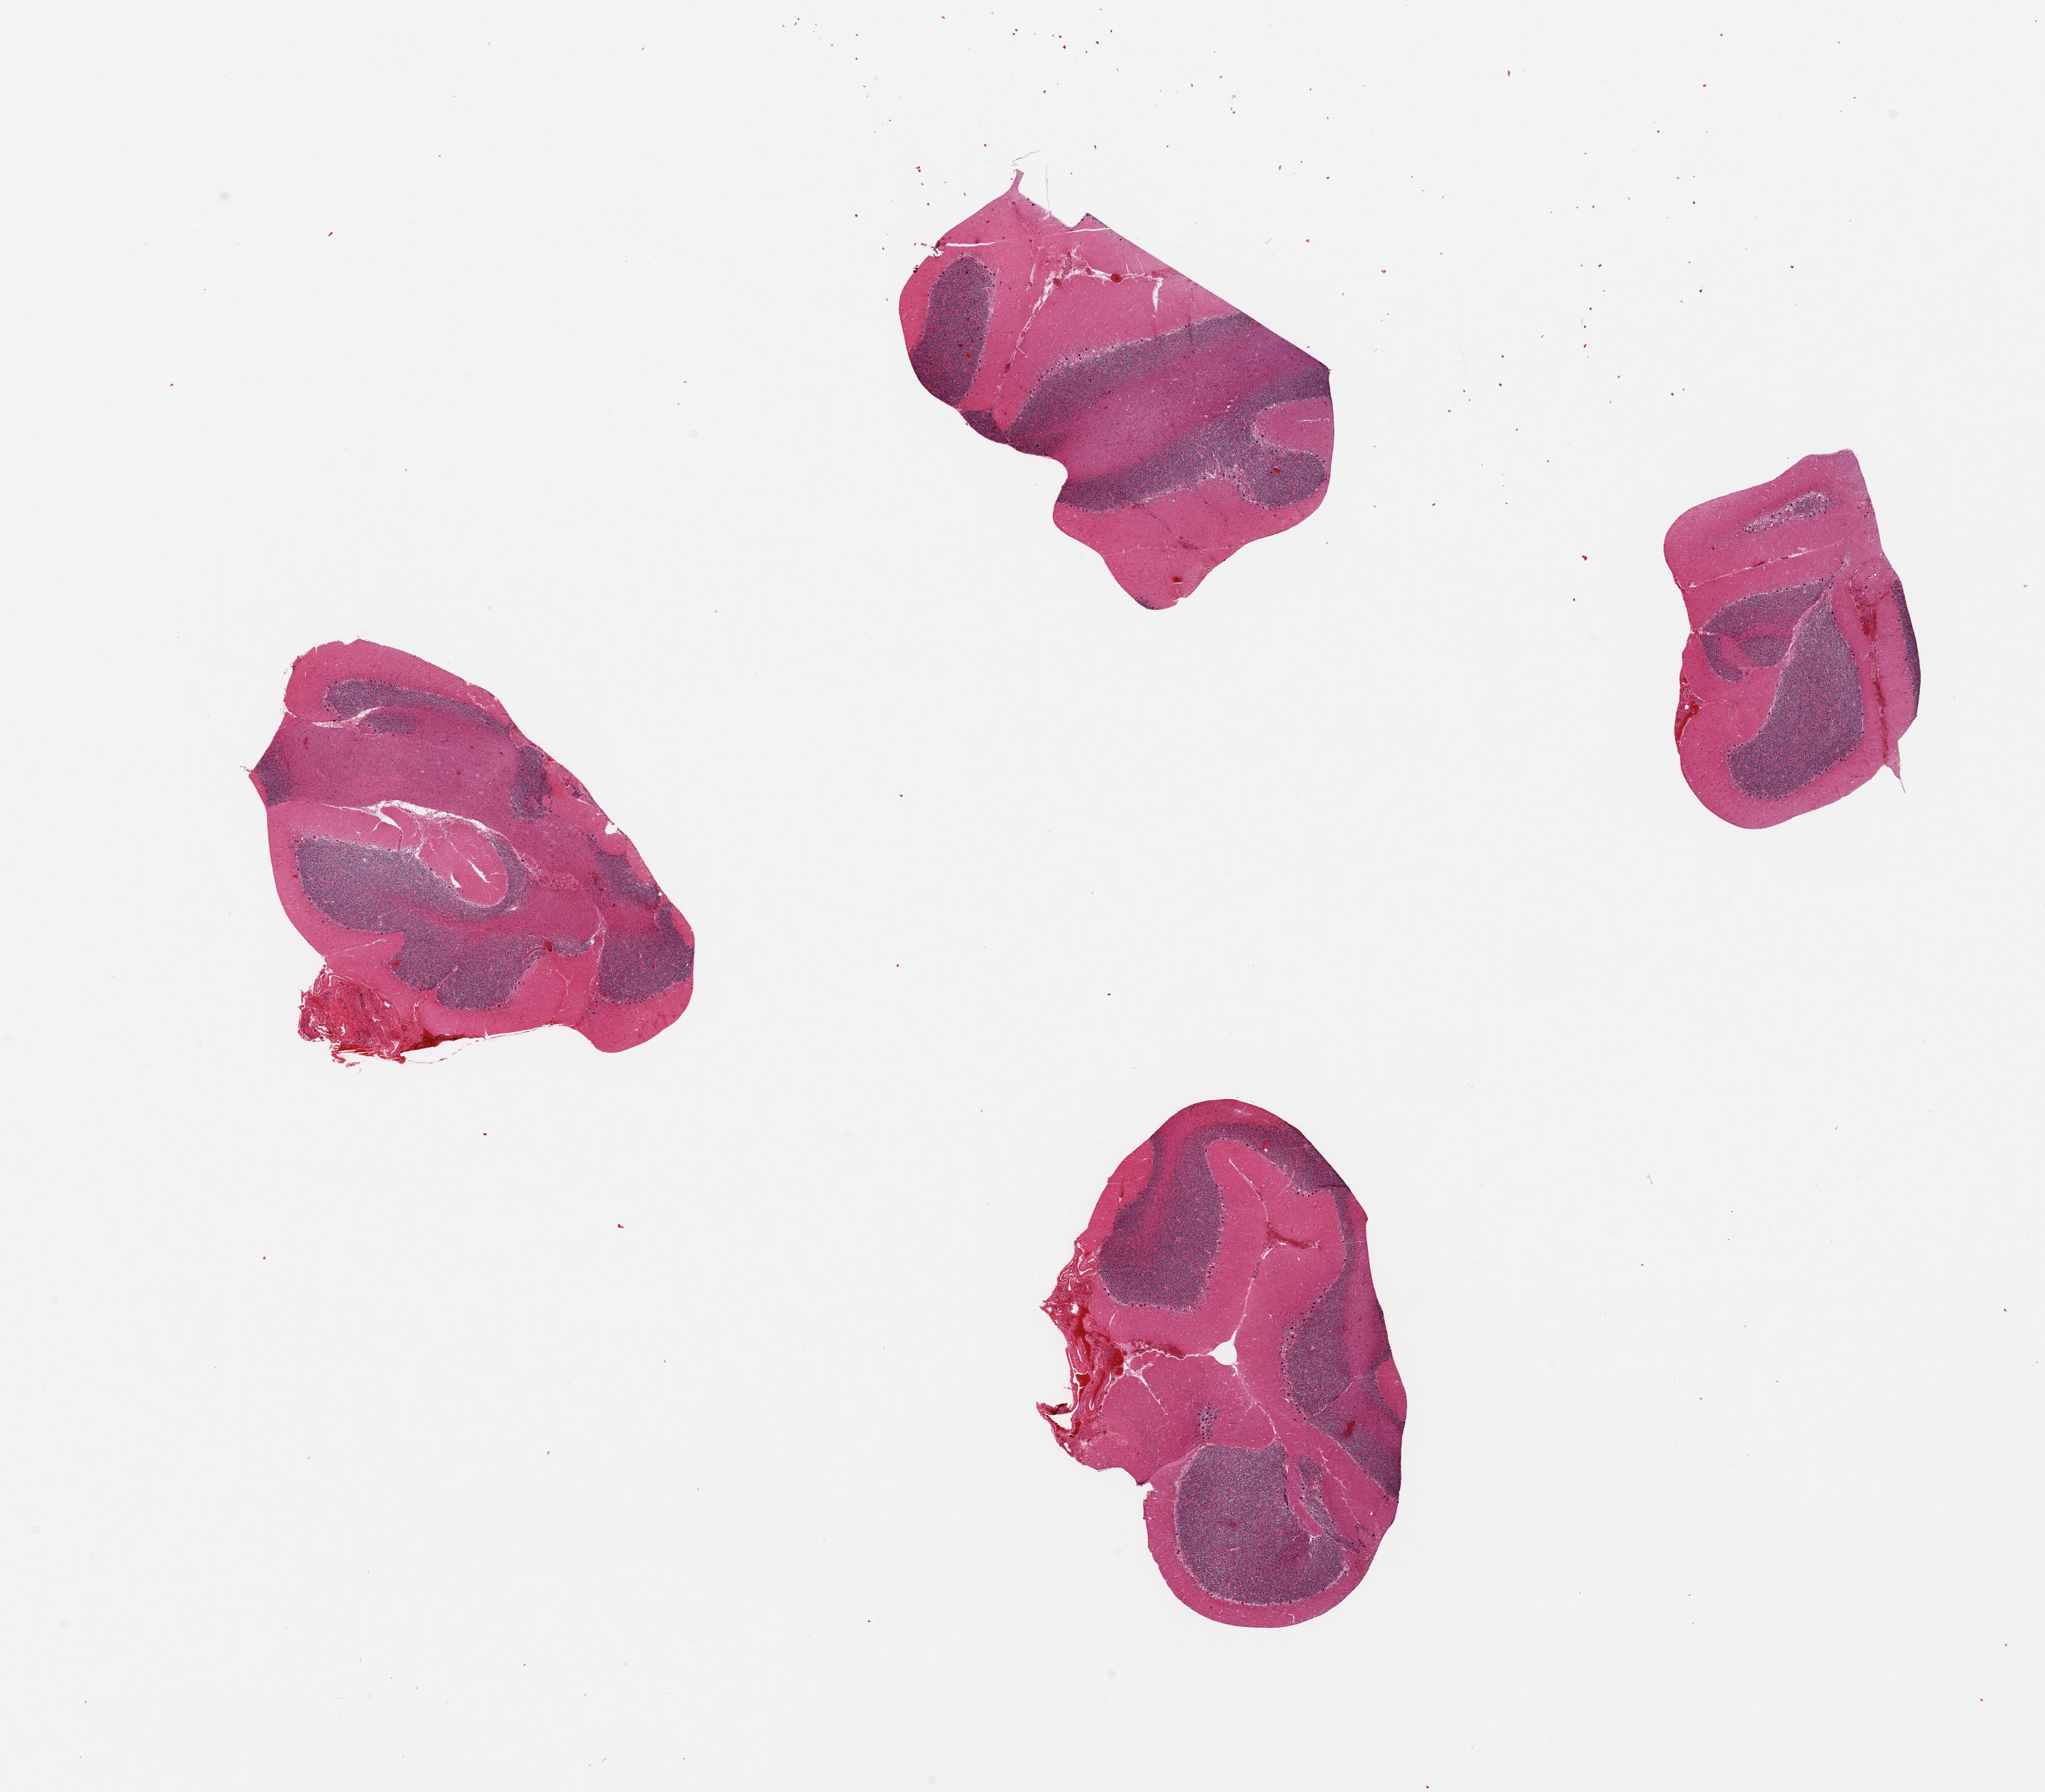
Digitized haematoxylin and eosin-stained section, low-resolution overview of the scanned area, about 22.6 x 19.8 mm; PAXgene-fixed, paraffin-embedded tissue; target tissue: cerebellum; tissue donor sample. Donor sex: male.
Pathologist's review note for this sample: 4 pieces; foci of adherent meninges.